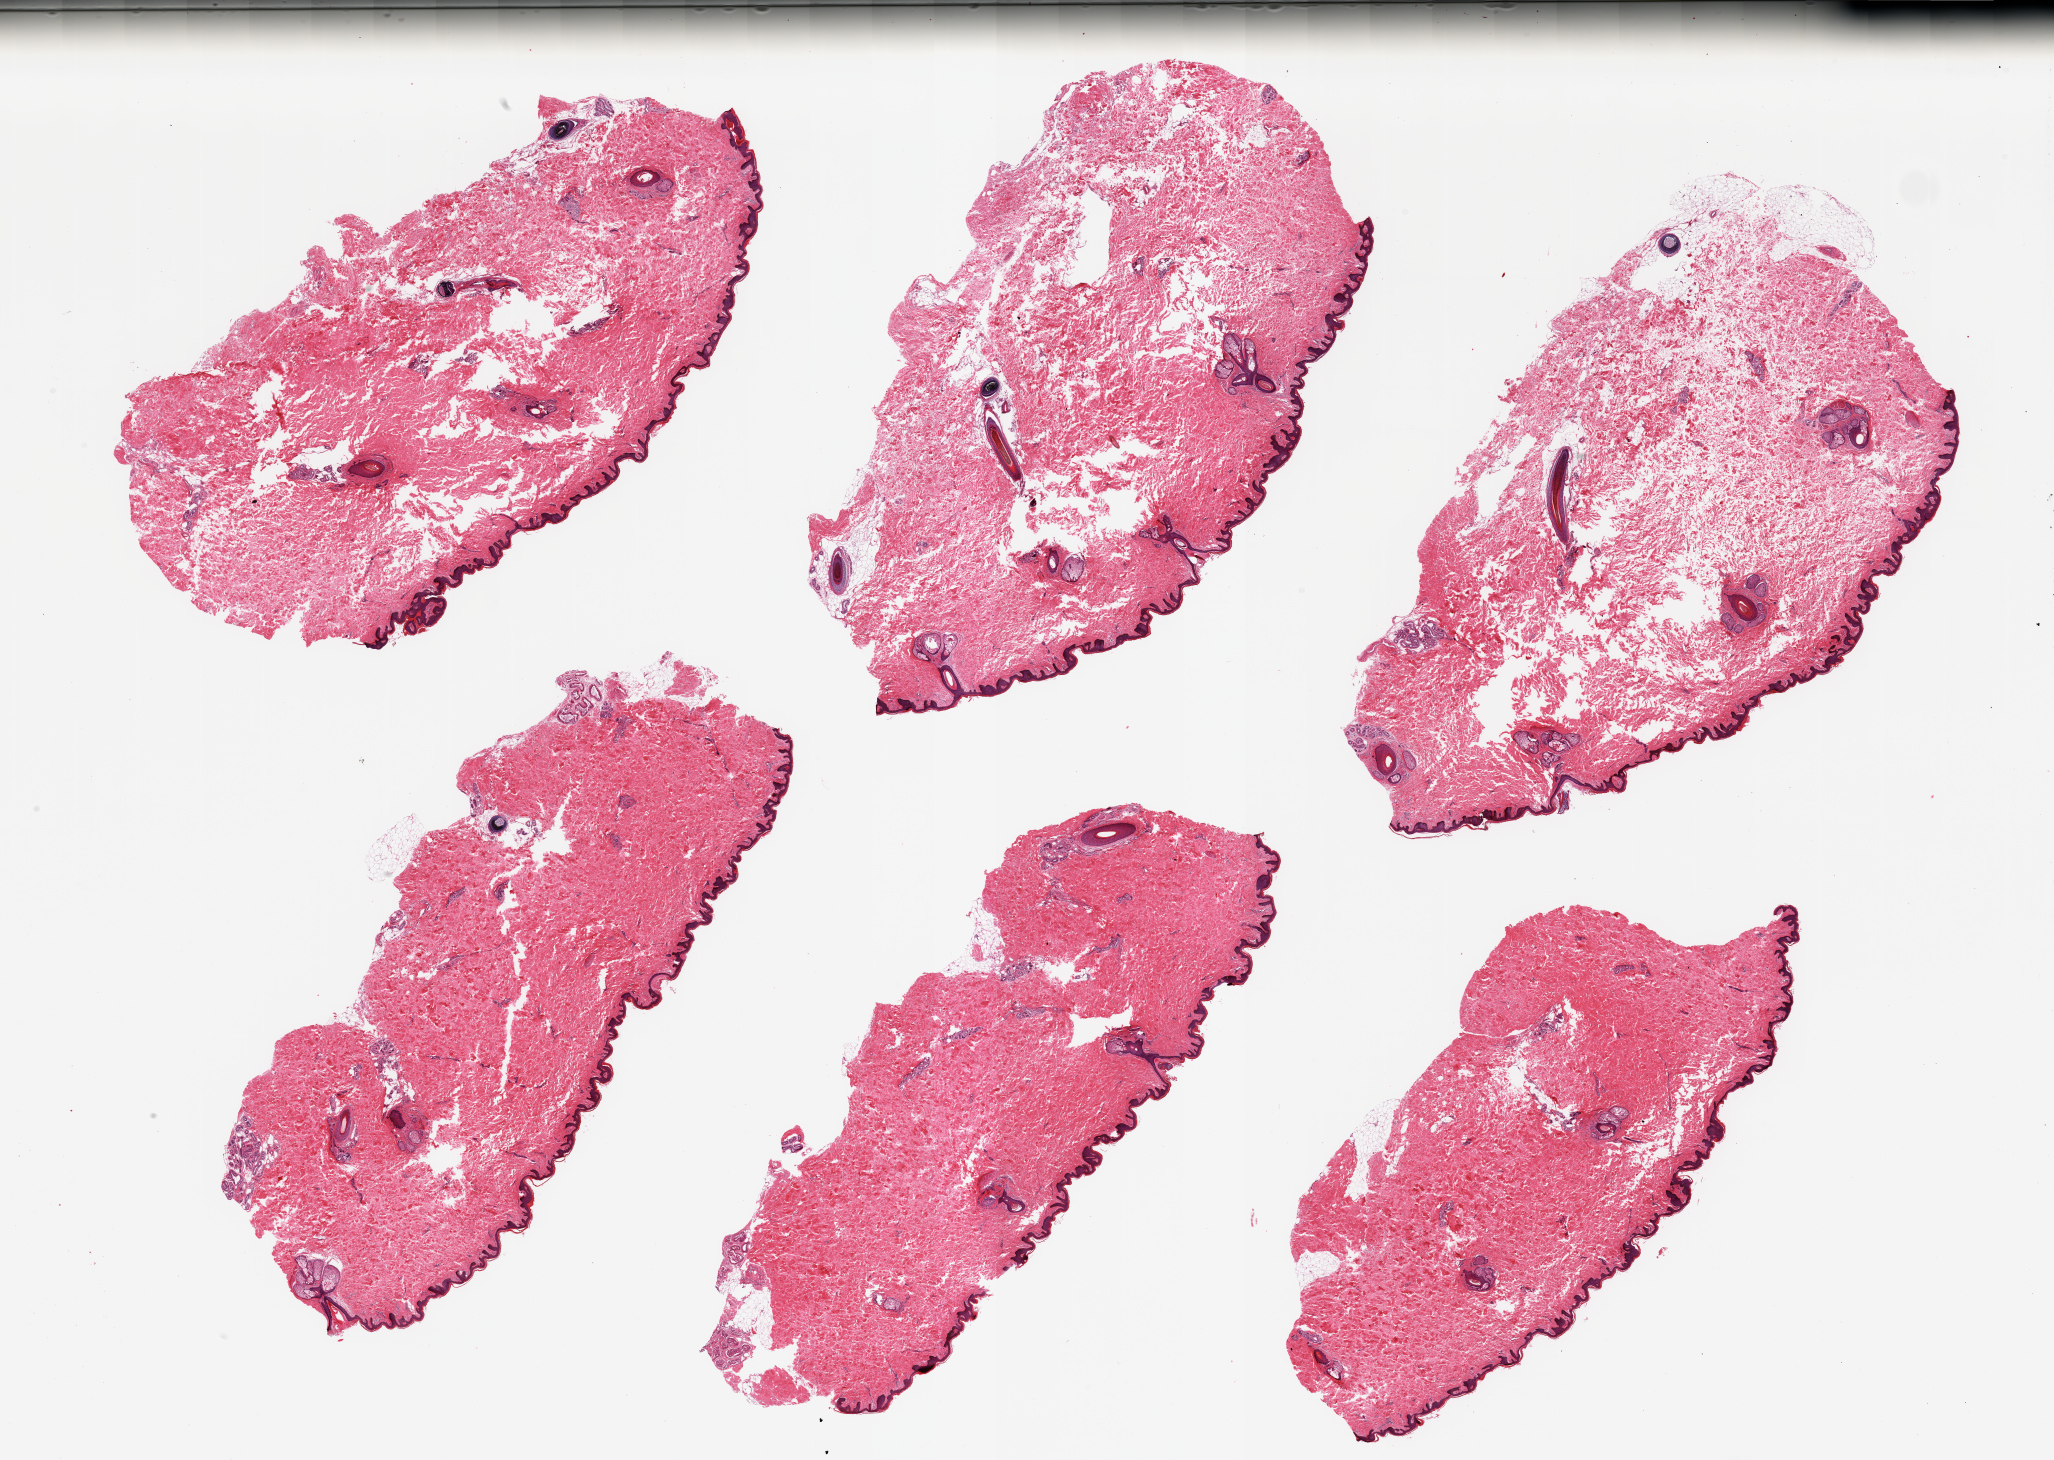
Hematoxylin and eosin (H&E) whole-slide image — a low-resolution overview of the entire scanned area, about 32.5 x 23.1 mm. PAXgene-fixed paraffin-embedded (PFPE) section. Sampled site (target tissue): skin of suprapubic region. Tissue donor sample. Donor sex: male.
• reviewer comment on this tissue sample: 6 pieces, trace dermal fat; squamous epithelium is ~35 microns